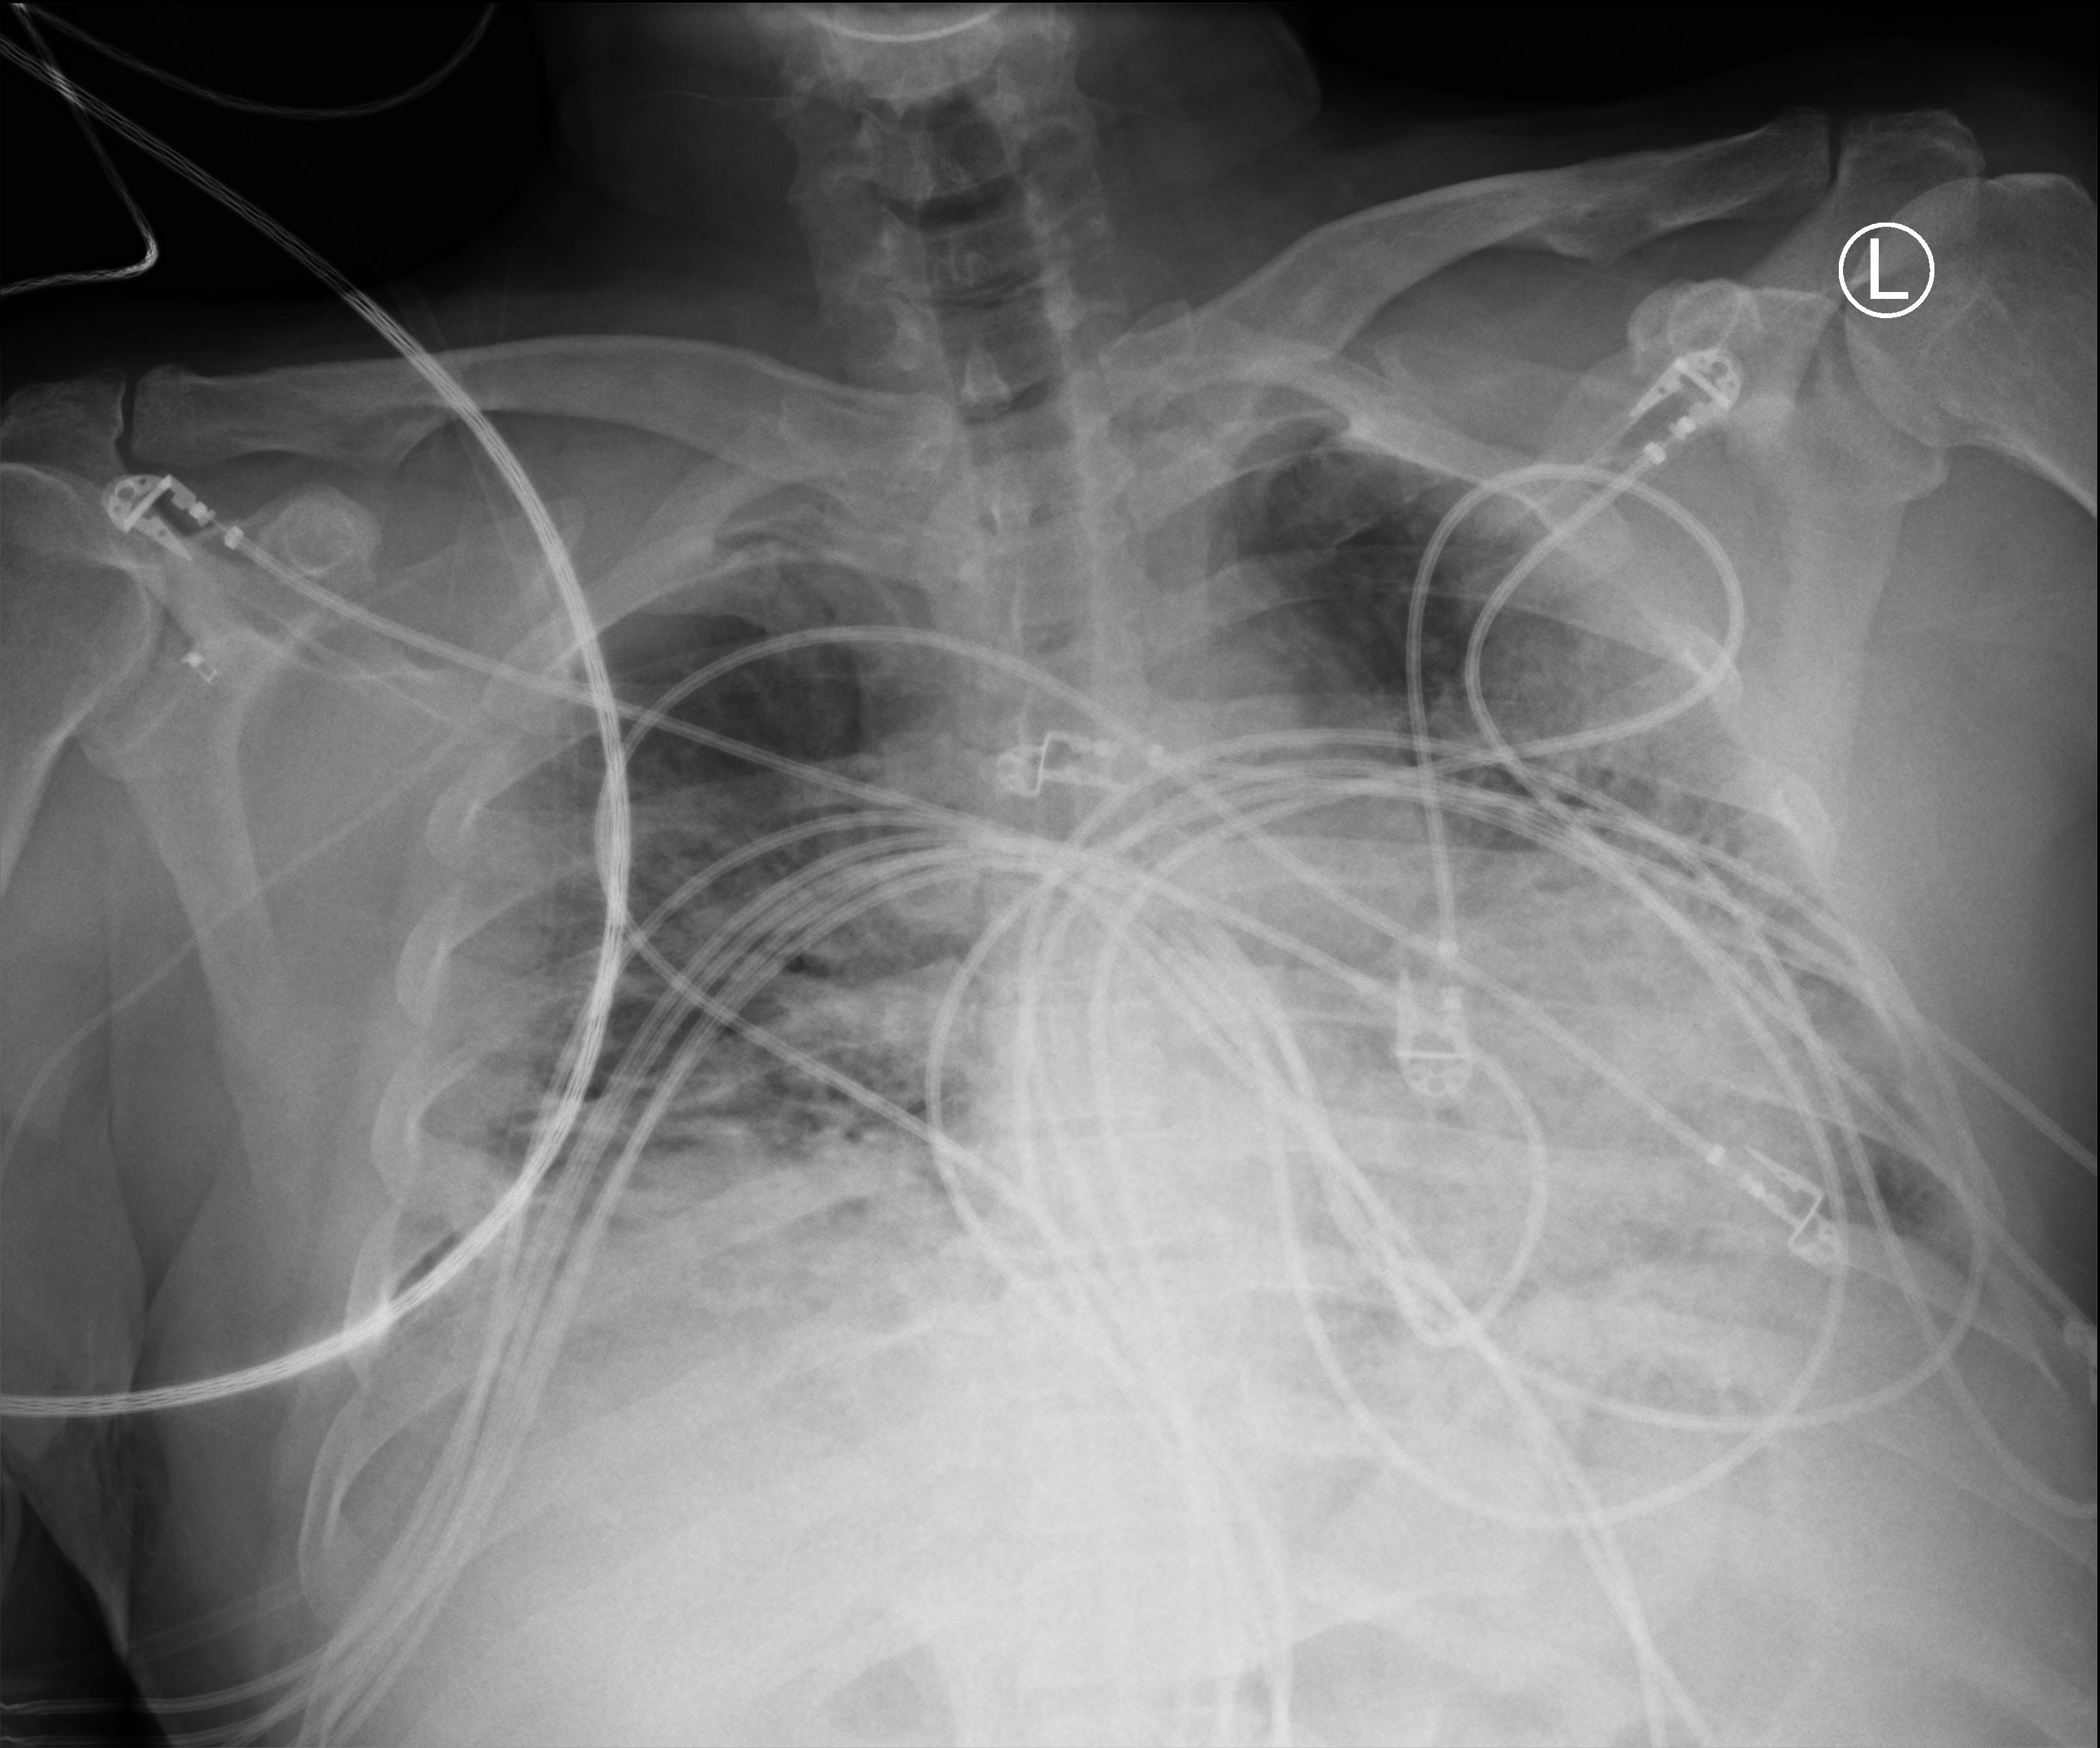
Bedside chest radiograph (computed radiography). Male patient hospitalised with COVID-19, age 18–59 years.
Admission-level facts for this patient (not findings on this image; timing relative to this image not recorded): smoking status (admission record): former.